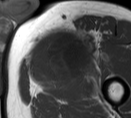
MRI of an extremity soft-tissue mass, one axial slice. MR volume resampled by the dataset authors to the PET/CT grid (not the native acquisition matrix). 131 × 118 image matrix, field of view 128 × 115 mm. Male patient. Case-level facts recorded for this patient, not image findings: histological type: pleiomorphic liposarcoma; grade: high; site of the primary tumour: left thigh.
Outlined on this slice (expert contour drawn on MRI and transferred to this co-registered scan by the dataset authors):
- gross tumour volume including surrounding oedema: bounding box [x1, y1, x2, y2] px = [32, 25, 97, 79]
- gross tumour volume (mass): [32, 34, 81, 76]